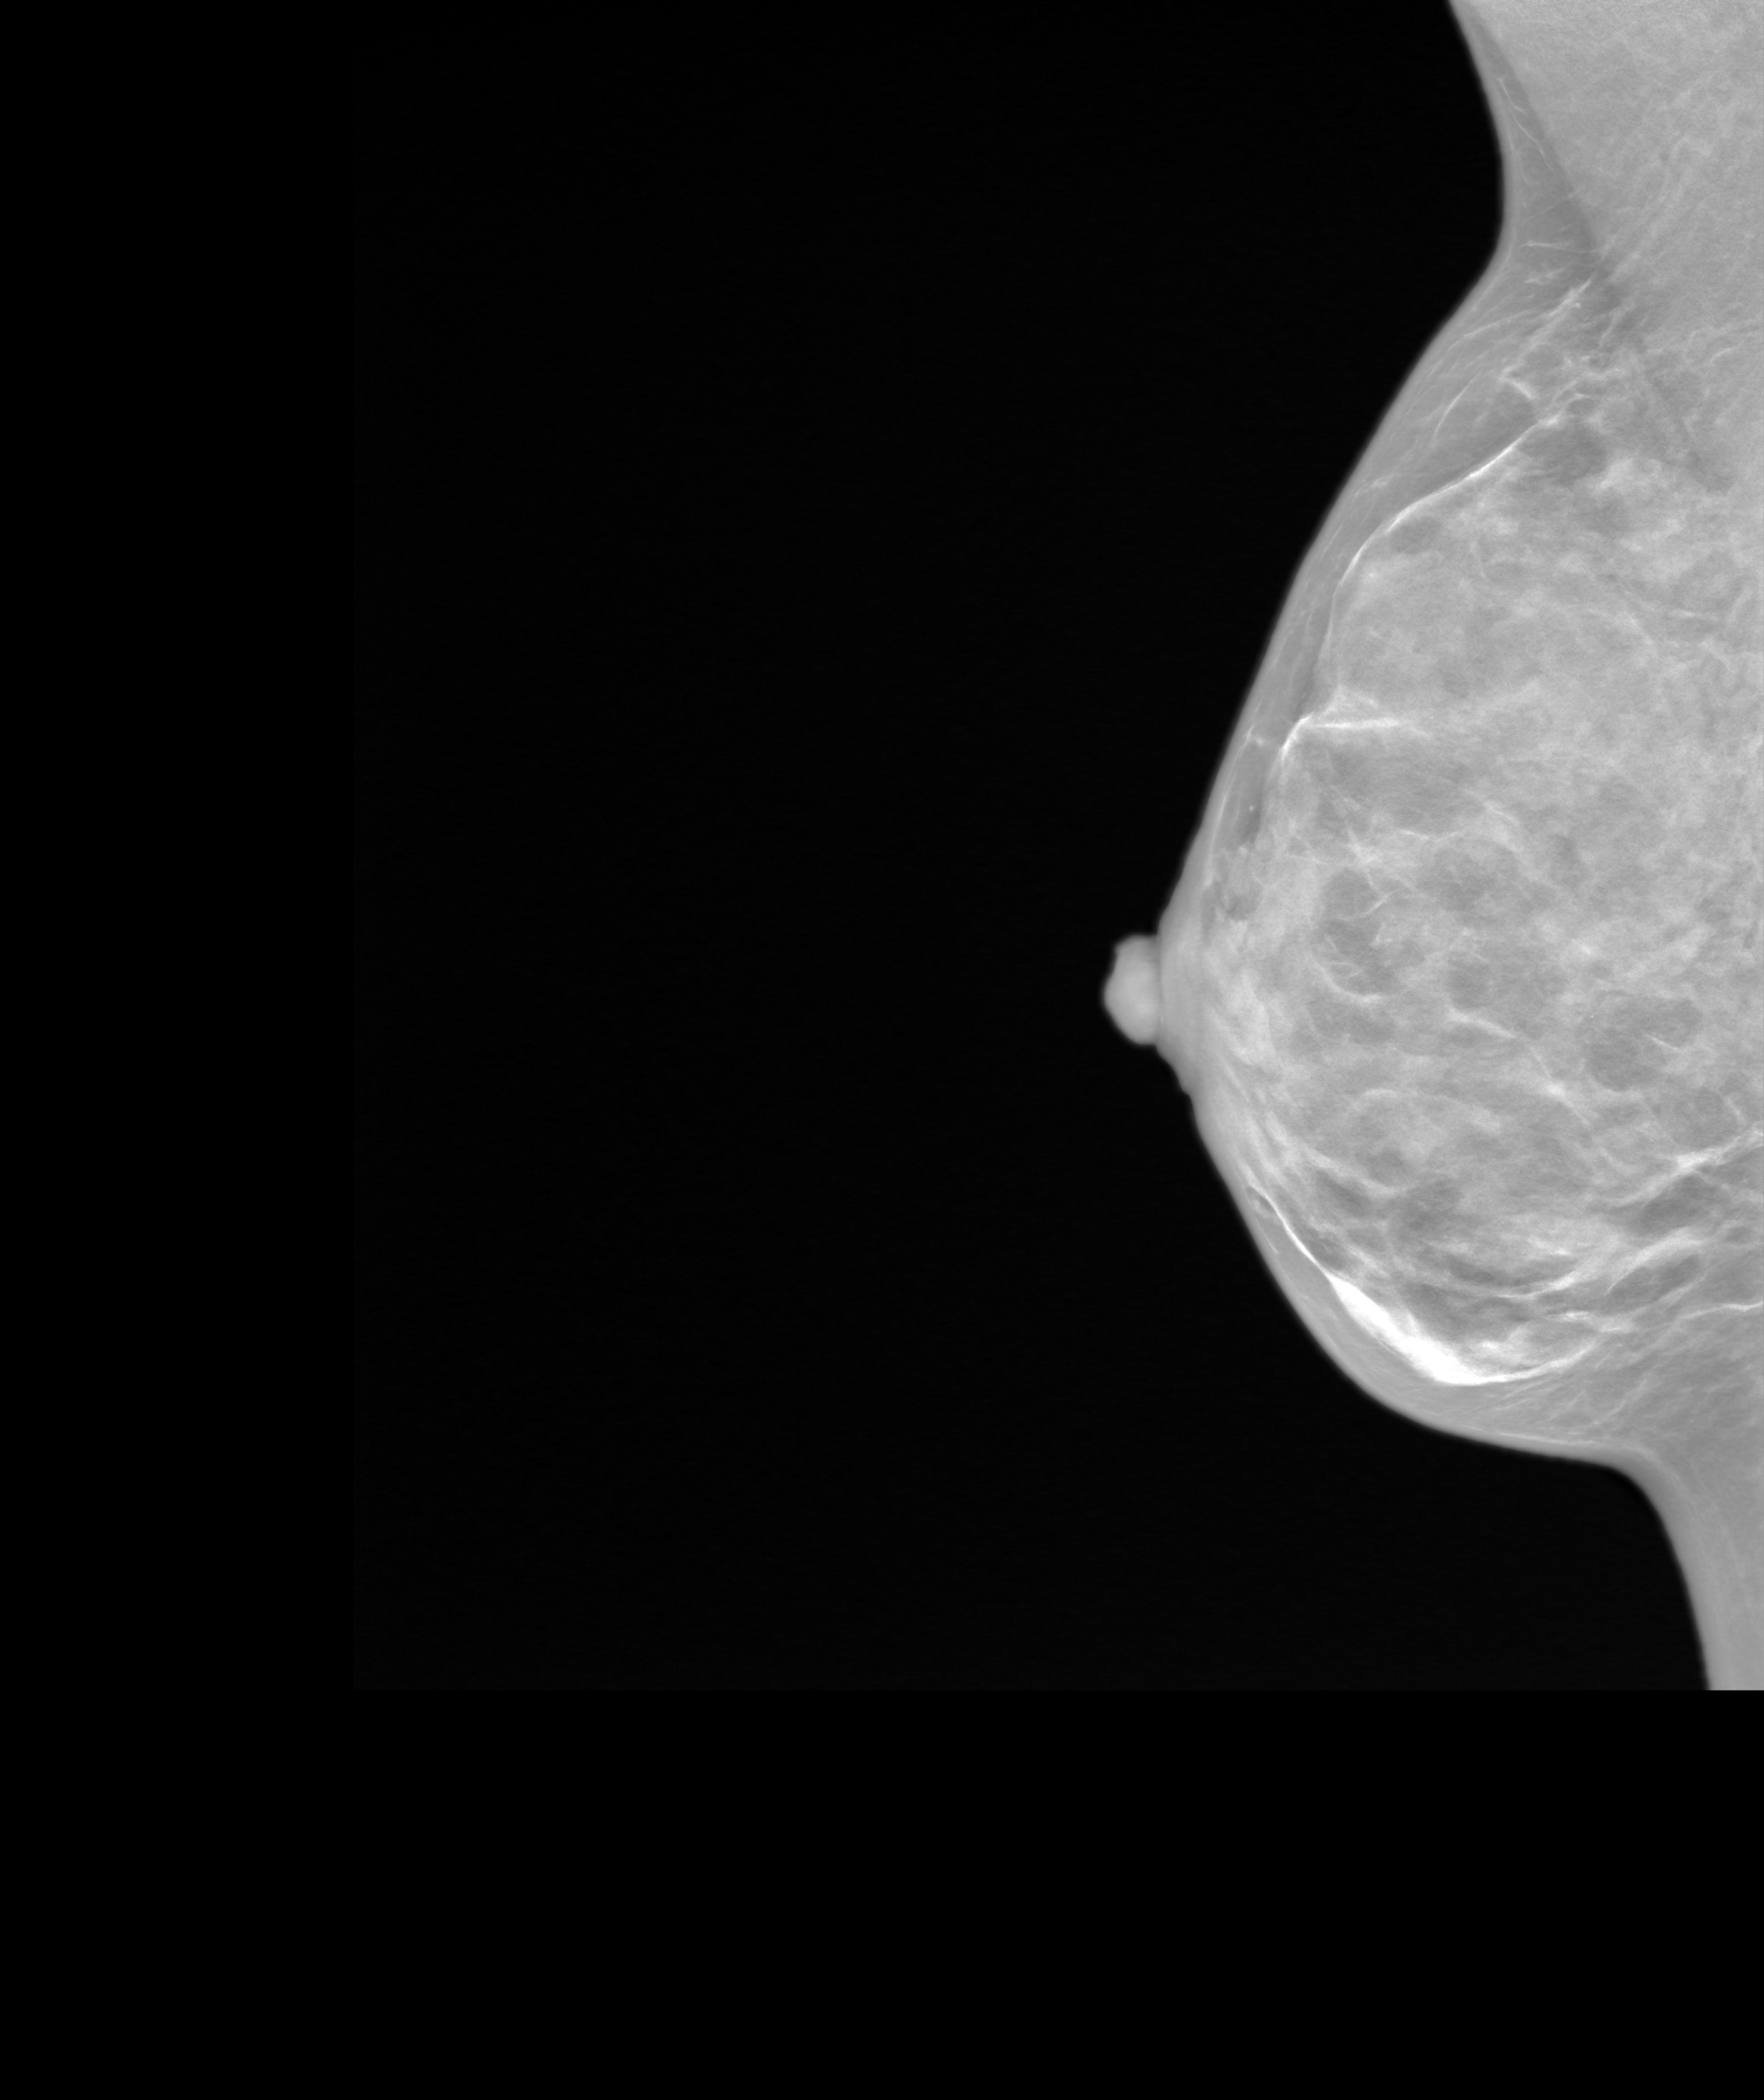
Screening examination. Patient aged 46 years (female).
Image type: synthesized 2-D view from tomosynthesis. Breast: right. Projection: medio-lateral oblique projection.